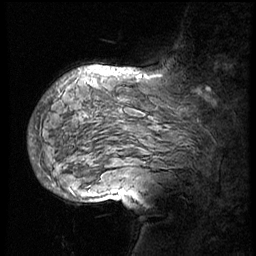
Breast MRI (dynamic contrast-enhanced), one sagittal slice. Slice 40 of 56 in the series (ordered by position). 3 images stored at this slice position (order not interpretable as contrast timing). 1.5 T. TE 4.2 ms, TR 8.9 ms. 3 mm slice thickness. 256 × 256 image matrix, field of view 220 × 220 mm. Patient: female, 57 years. From the clinical record (not read from this slice): setting: breast cancer imaged before/during neoadjuvant chemotherapy; receptor status: HER2-positive.
Outlined on this slice (semi-automatic segmentation, software-assisted and operator-edited):
- analysis volume of interest (the breast-tissue region the enhancement analysis was run in; not a lesion): bounding box (x1, y1, x2, y2) in pixels: (29, 70, 228, 156)
- tumour enhancement mask (voxels above the 140 % enhancement threshold inside the analysis volume of interest): (65, 70, 115, 84)